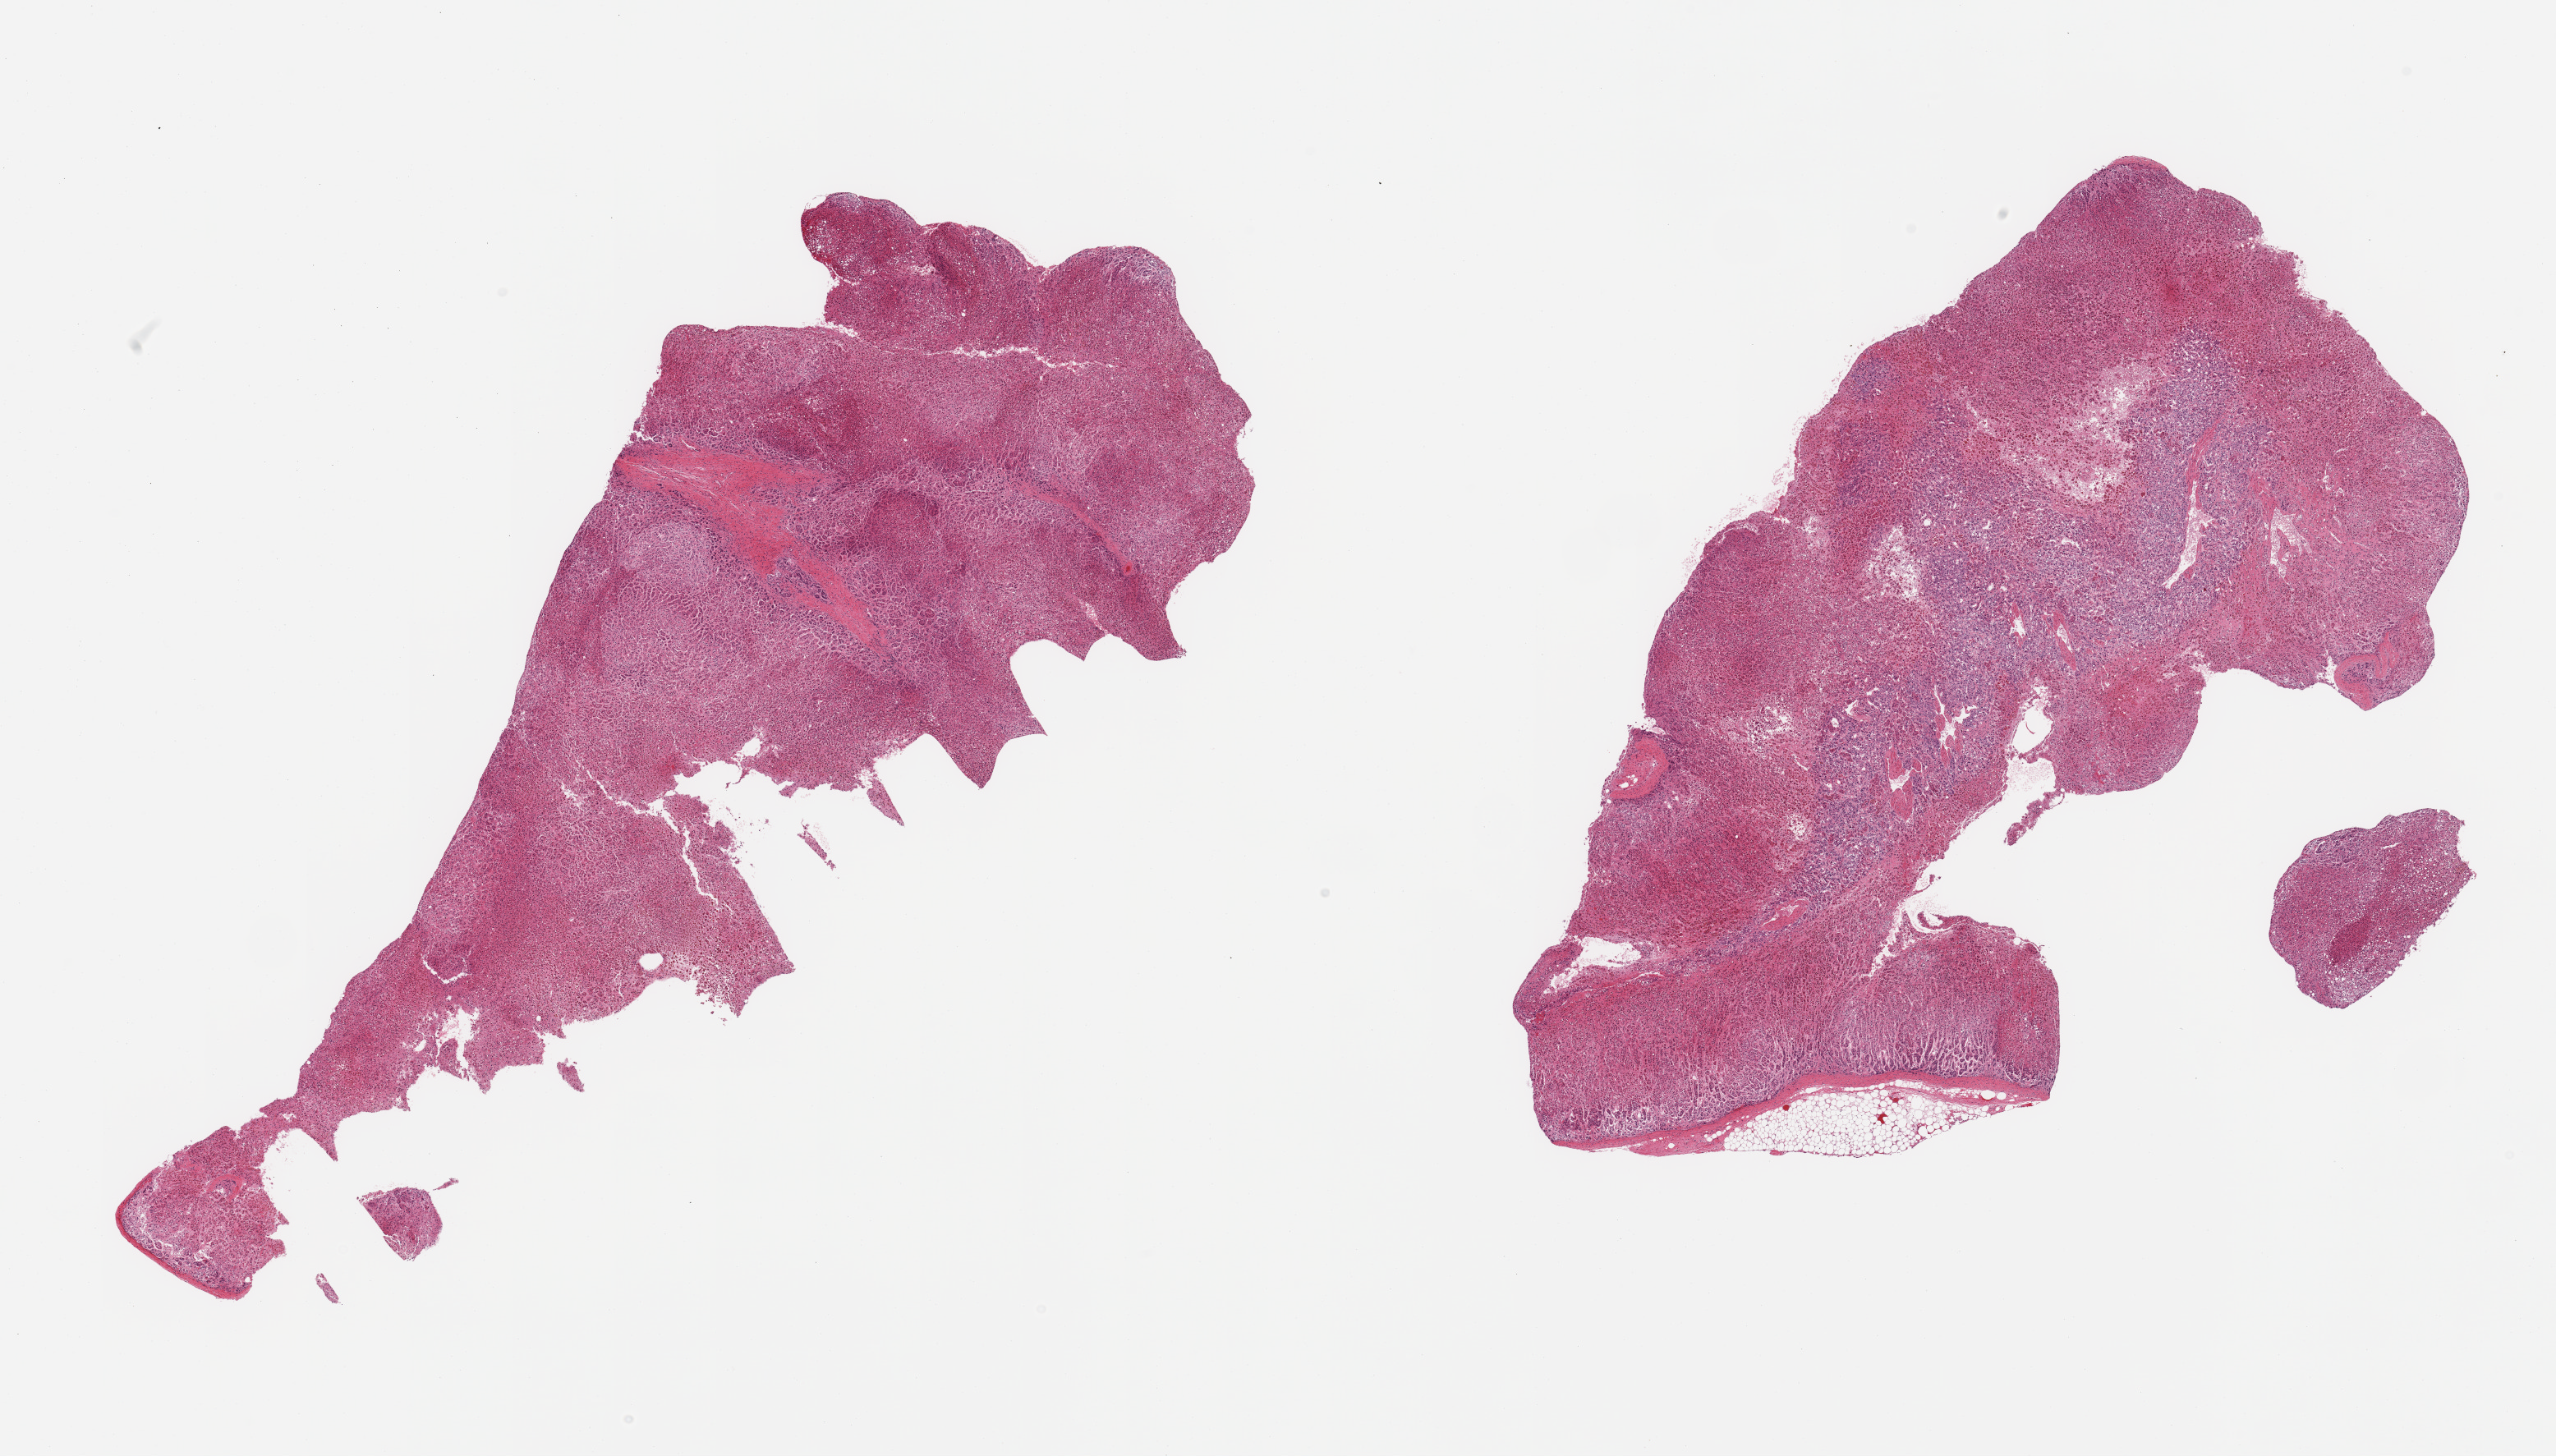
Whole-slide image, haematoxylin and eosin stain — whole scanned area (about 24.6 x 14.0 mm, from a 20x scan) shown as a low-resolution overview. PAXgene-fixed, paraffin-embedded tissue. Target tissue: adrenal gland. Tissue donor sample.
- reviewer comment on this tissue sample: 2 pieces: mildly to moderatly autolyzed adrenal cortex and medulla, attached minute fragment of external fat